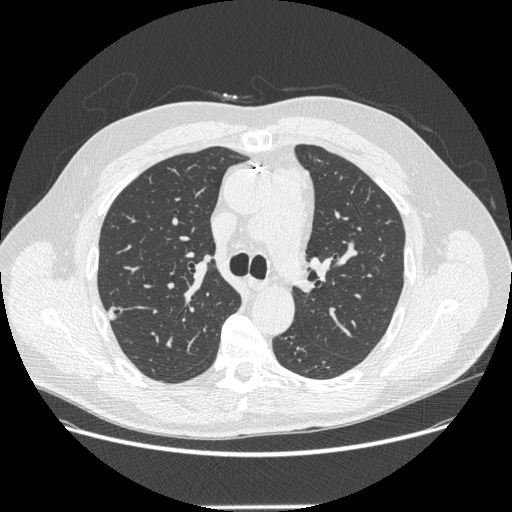
Low-dose screening chest CT, axial slice; third screening round (two years after baseline); lung window (W 1500 / L -600 HU); 1.25 mm slice thickness; standard (soft-tissue) reconstruction kernel (STANDARD); 512 × 512 image matrix. Male participant, aged 62 years at enrolment.
Expert-annotated lung lesion, box from (x=94, y=299) to (x=133, y=333) px. The exam's reader record, not a measurement of the box and not confirmed to be the same lesion: non-calcified nodule or mass ≥4 mm, right upper lobe, 12 × 11 mm, smooth margins, soft tissue attenuation, pre-existing on the prior screen: yes; interval growth: yes. Official screen result: positive, other. Later outcome: lung cancer diagnosed 112 days after this screen — adenocarcinoma, NOS, right upper lobe, moderately differentiated (G2), stage IA (AJCC 6th edition), 12 mm at pathology.